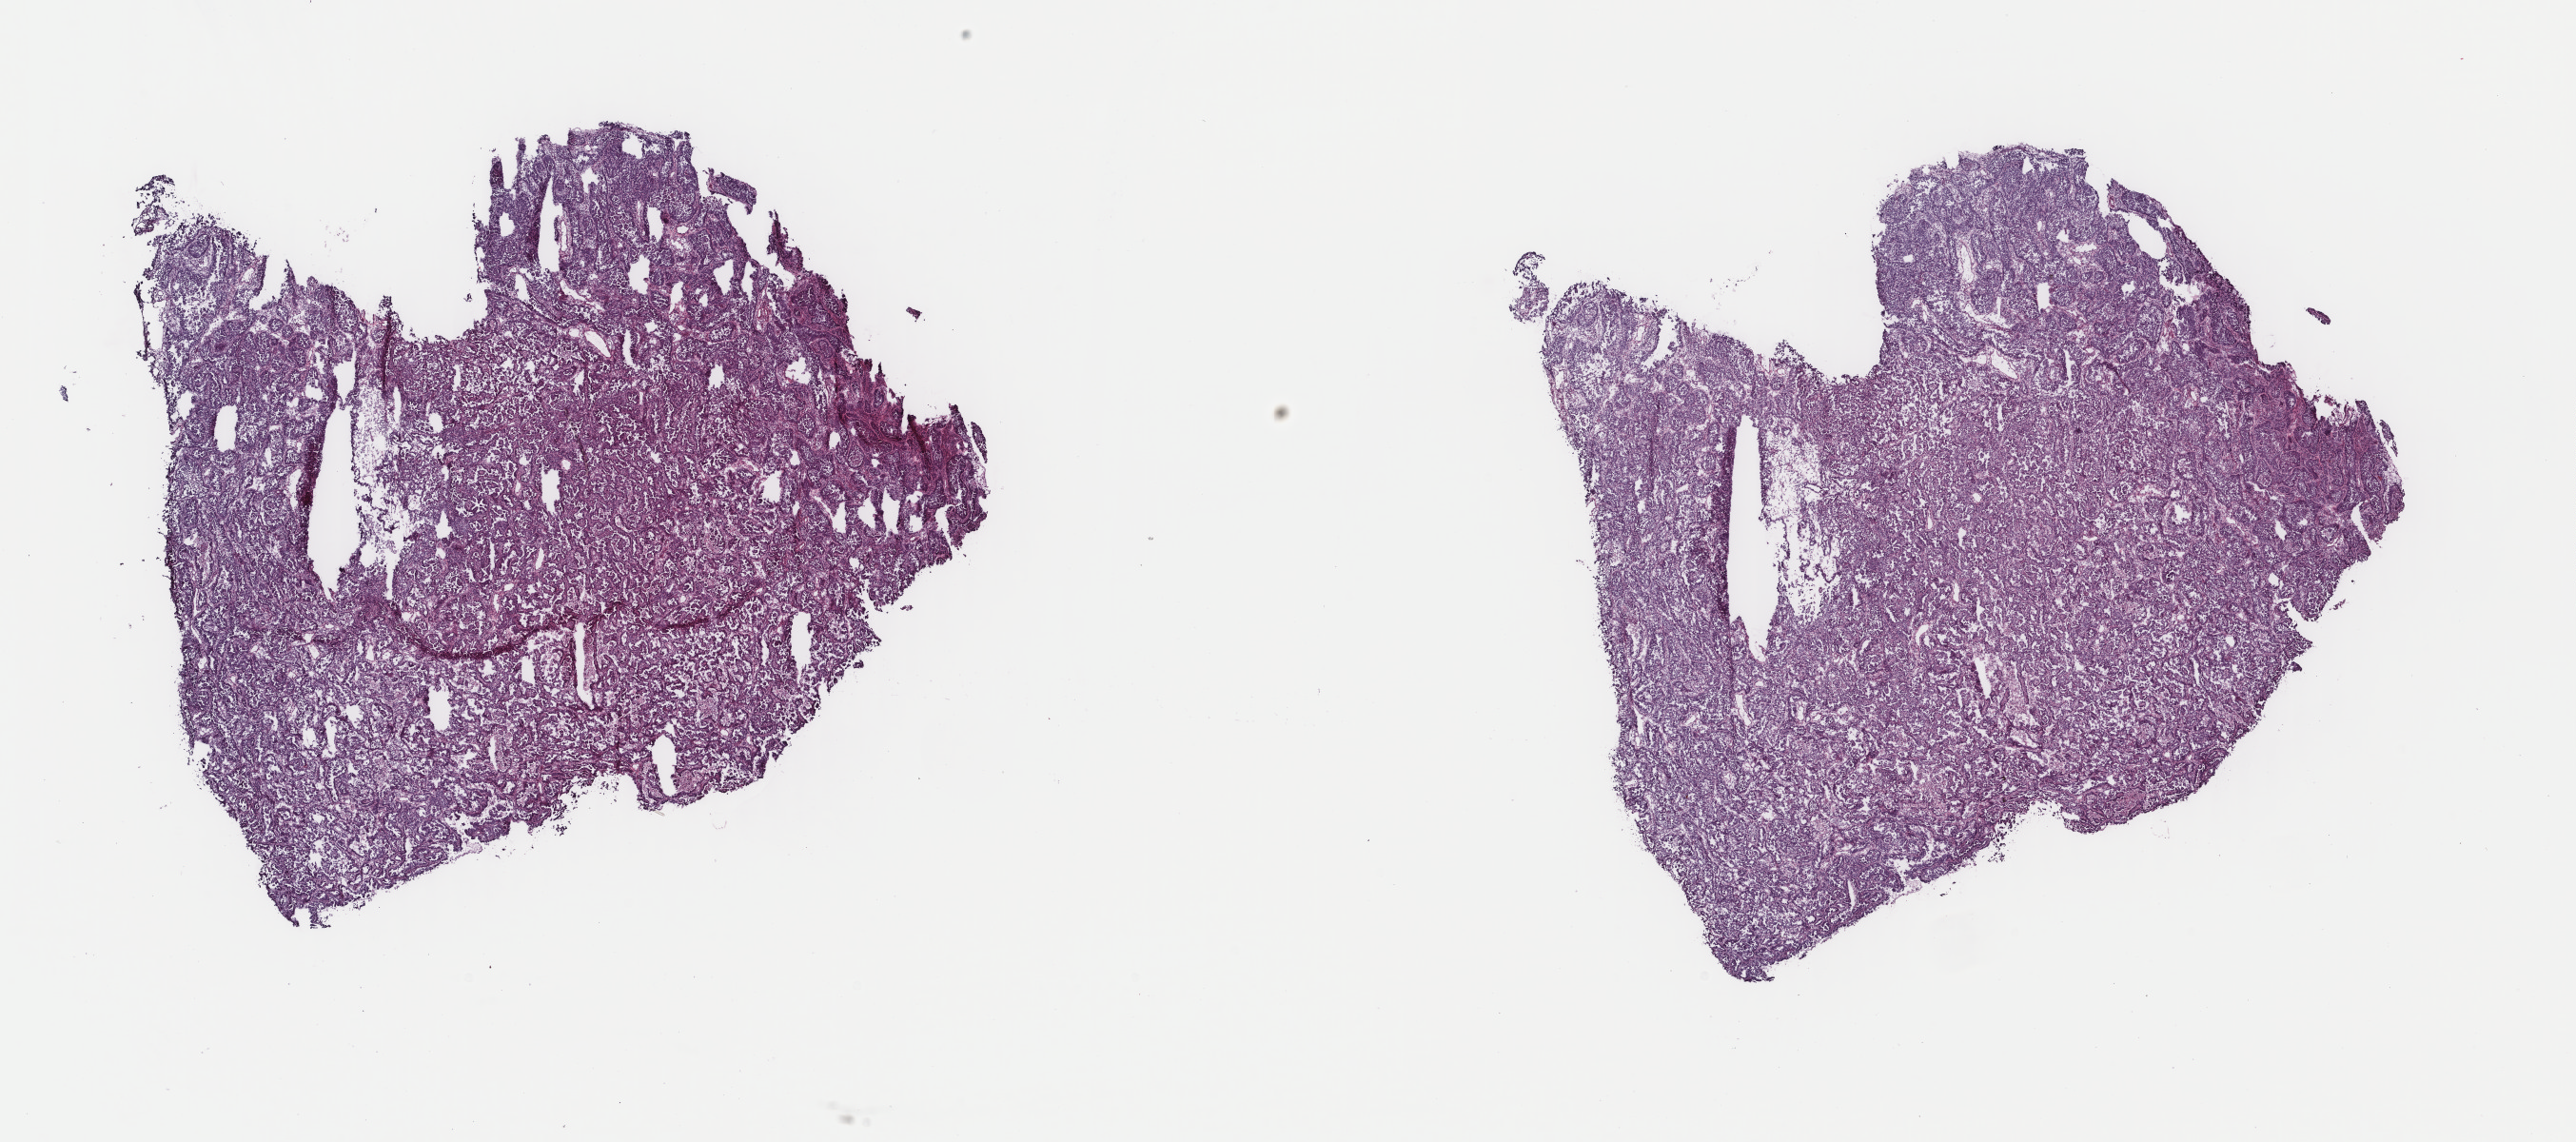
Whole-slide histology image, Hematoxylin and eosin (H&E) stained — whole scanned area (about 21.5 x 9.5 mm) shown as a low-resolution overview. Frozen section. Uterus, primary tumour sample. Patient: female, age at initial diagnosis 67 years. Histologic grade: G3 (poorly differentiated). Pathologist review of this section (percent, as recorded): tumour cells 80%, tumour nuclei 85%, normal cells 0%, stromal cells 15%, necrosis 5%. Inflammatory infiltration, as recorded: lymphocyte infiltration 2%, monocyte infiltration 2%, neutrophil infiltration 2%.
FIGO stage: IIIC. Histologic diagnosis: Serous cystadenocarcinoma, NOS.